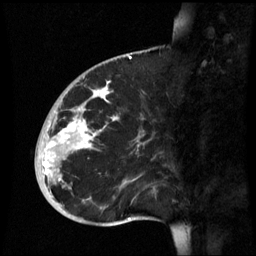
Breast MRI (dynamic contrast-enhanced), one sagittal slice; position 22 of 60 along the scan axis; dynamic contrast-enhanced series, image 2 of 3 at this slice position (ordered by acquisition); 1.5 T; TE 4.2 ms, TR 8.9 ms; 2.6 mm slice thickness; 256 × 256 image matrix. Female patient, age 35 years. Case-level facts recorded for this patient, not image findings: setting: breast cancer imaged before/during neoadjuvant chemotherapy; receptor status: HR-positive, HER2-negative.
Structures marked on this image (semi-automatic segmentation, software-assisted and operator-edited):
- analysis volume of interest (the breast-tissue region the enhancement analysis was run in; not a lesion): bounding box [x1, y1, x2, y2] px = [35, 74, 162, 221]
- tumour enhancement mask (voxels above the 70 % enhancement threshold inside the analysis volume of interest): [42, 82, 117, 181]